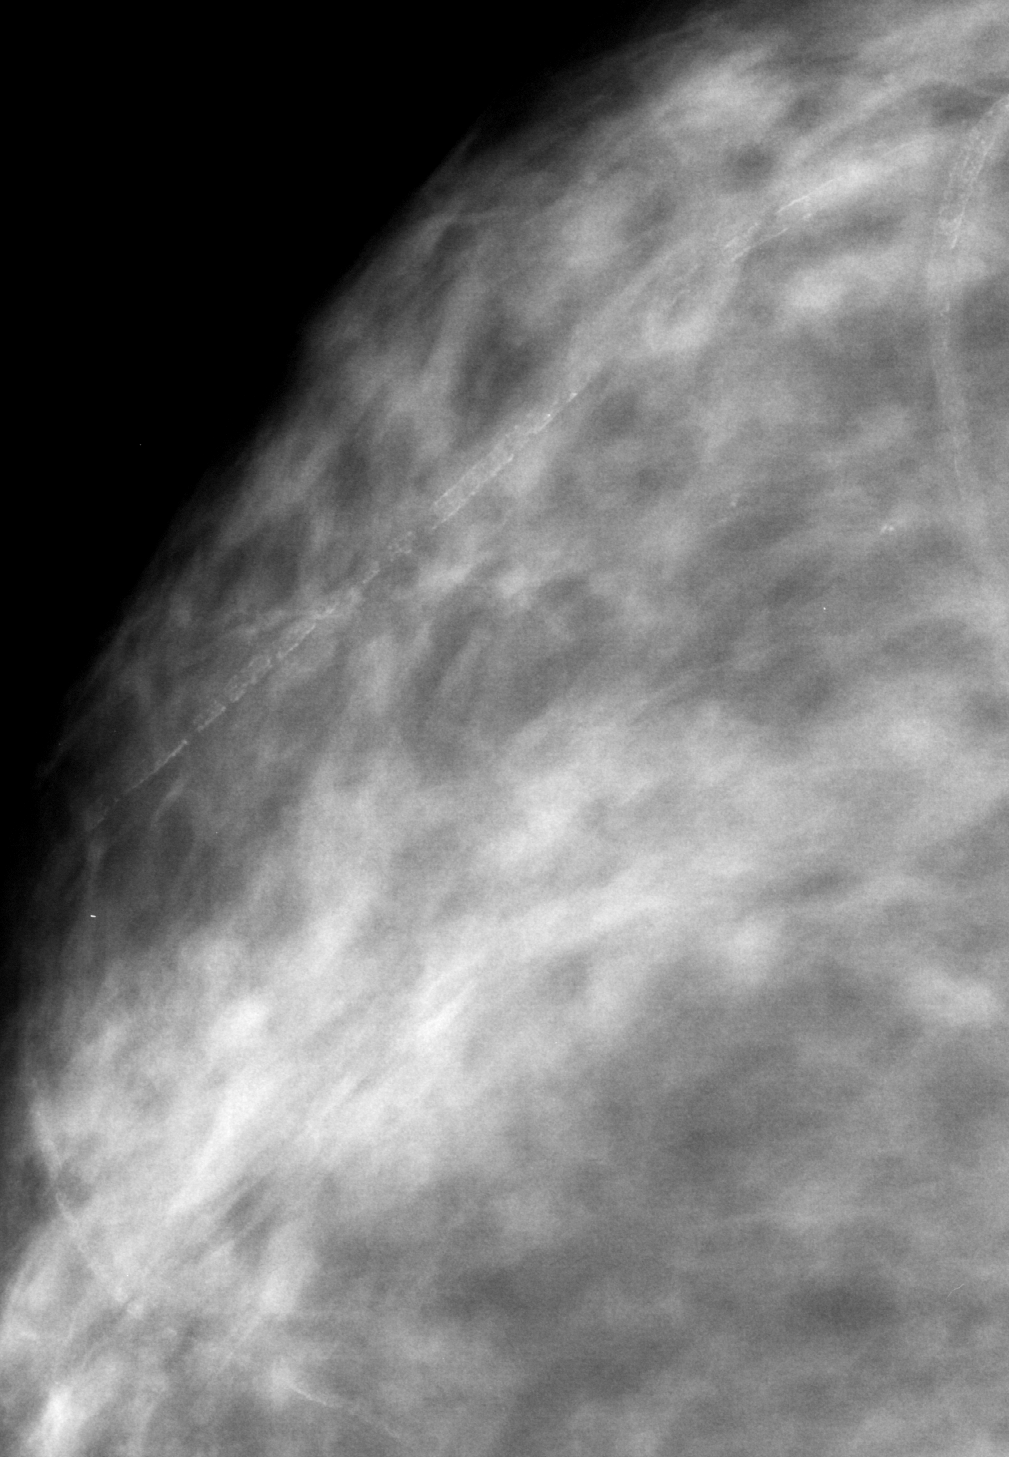
Cropped region of a digitized screen-film mammogram centred on a radiologist-marked abnormality, right breast, CC view, BI-RADS breast density category 2 (scale 1–4).
- Finding: calcifications, morphology vascular; BI-RADS assessment category 2; subtlety rating 4 on a 1 (subtle) to 5 (obvious) scale; benign without callback (not worked up further).